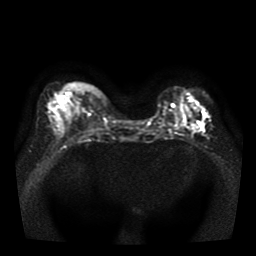
Breast MRI, one axial slice; position 14 of 41 along the scan axis; diffusion-weighted series; image 2 of 4 stored at this slice position (different b-values; order by instance number); 1.5 T; 5 mm slice thickness; 256 × 256 image matrix. Female patient.
Outlined on this slice (outlined manually by an expert reader):
- tumour on diffusion-weighted imaging: bounding box (x1, y1, x2, y2) in pixels: (190, 121, 195, 126)